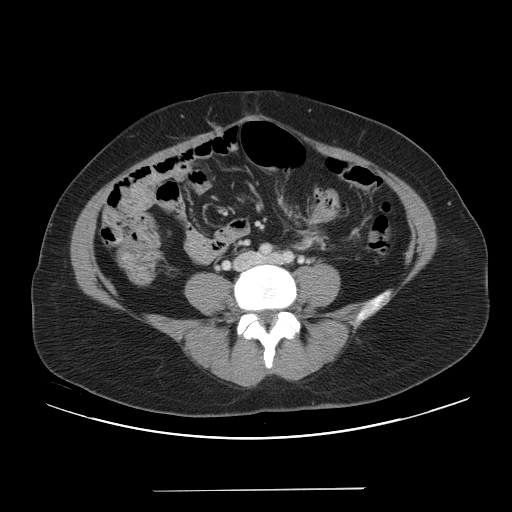
Contrast-enhanced abdominal CT, one axial slice; slice 1 of 56 in the series (ordered by position); 120 kVp; intravenous contrast given; soft-tissue window (W 400 / L 40 HU); 512 × 512 image matrix, field of view 419 × 419 mm. Female patient, age 54 years. Case-level facts recorded for this patient, not image findings: diagnosis: colorectal cancer liver metastases, imaged before liver resection; multiple liver metastases: yes; largest metastasis: 3.2 cm; chemotherapy before resection: yes.
Annotated regions visible in this slice (manually delineated by an expert):
- liver: bounding box (x1, y1, x2, y2) in pixels: (104, 211, 112, 226)